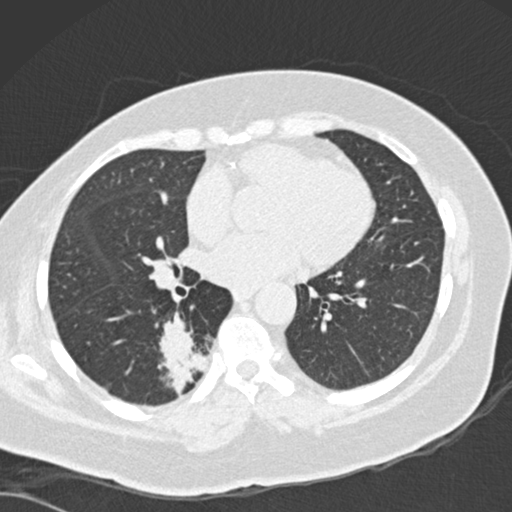
Chest CT (low-dose screening protocol), one axial image, first (baseline) screen, lung window (W 1500 / L -600 HU), 2 mm slice thickness. Female participant, aged 66 years at enrolment. Current smoker at enrolment.
• Expert reader's lesion annotation, bounding box <152,322,225,396> (left, top, right, bottom; pixels).
• The screening reader recorded 3 non-calcified nodules or masses ≥4 mm on this exam; which of them this box marks is not recorded.